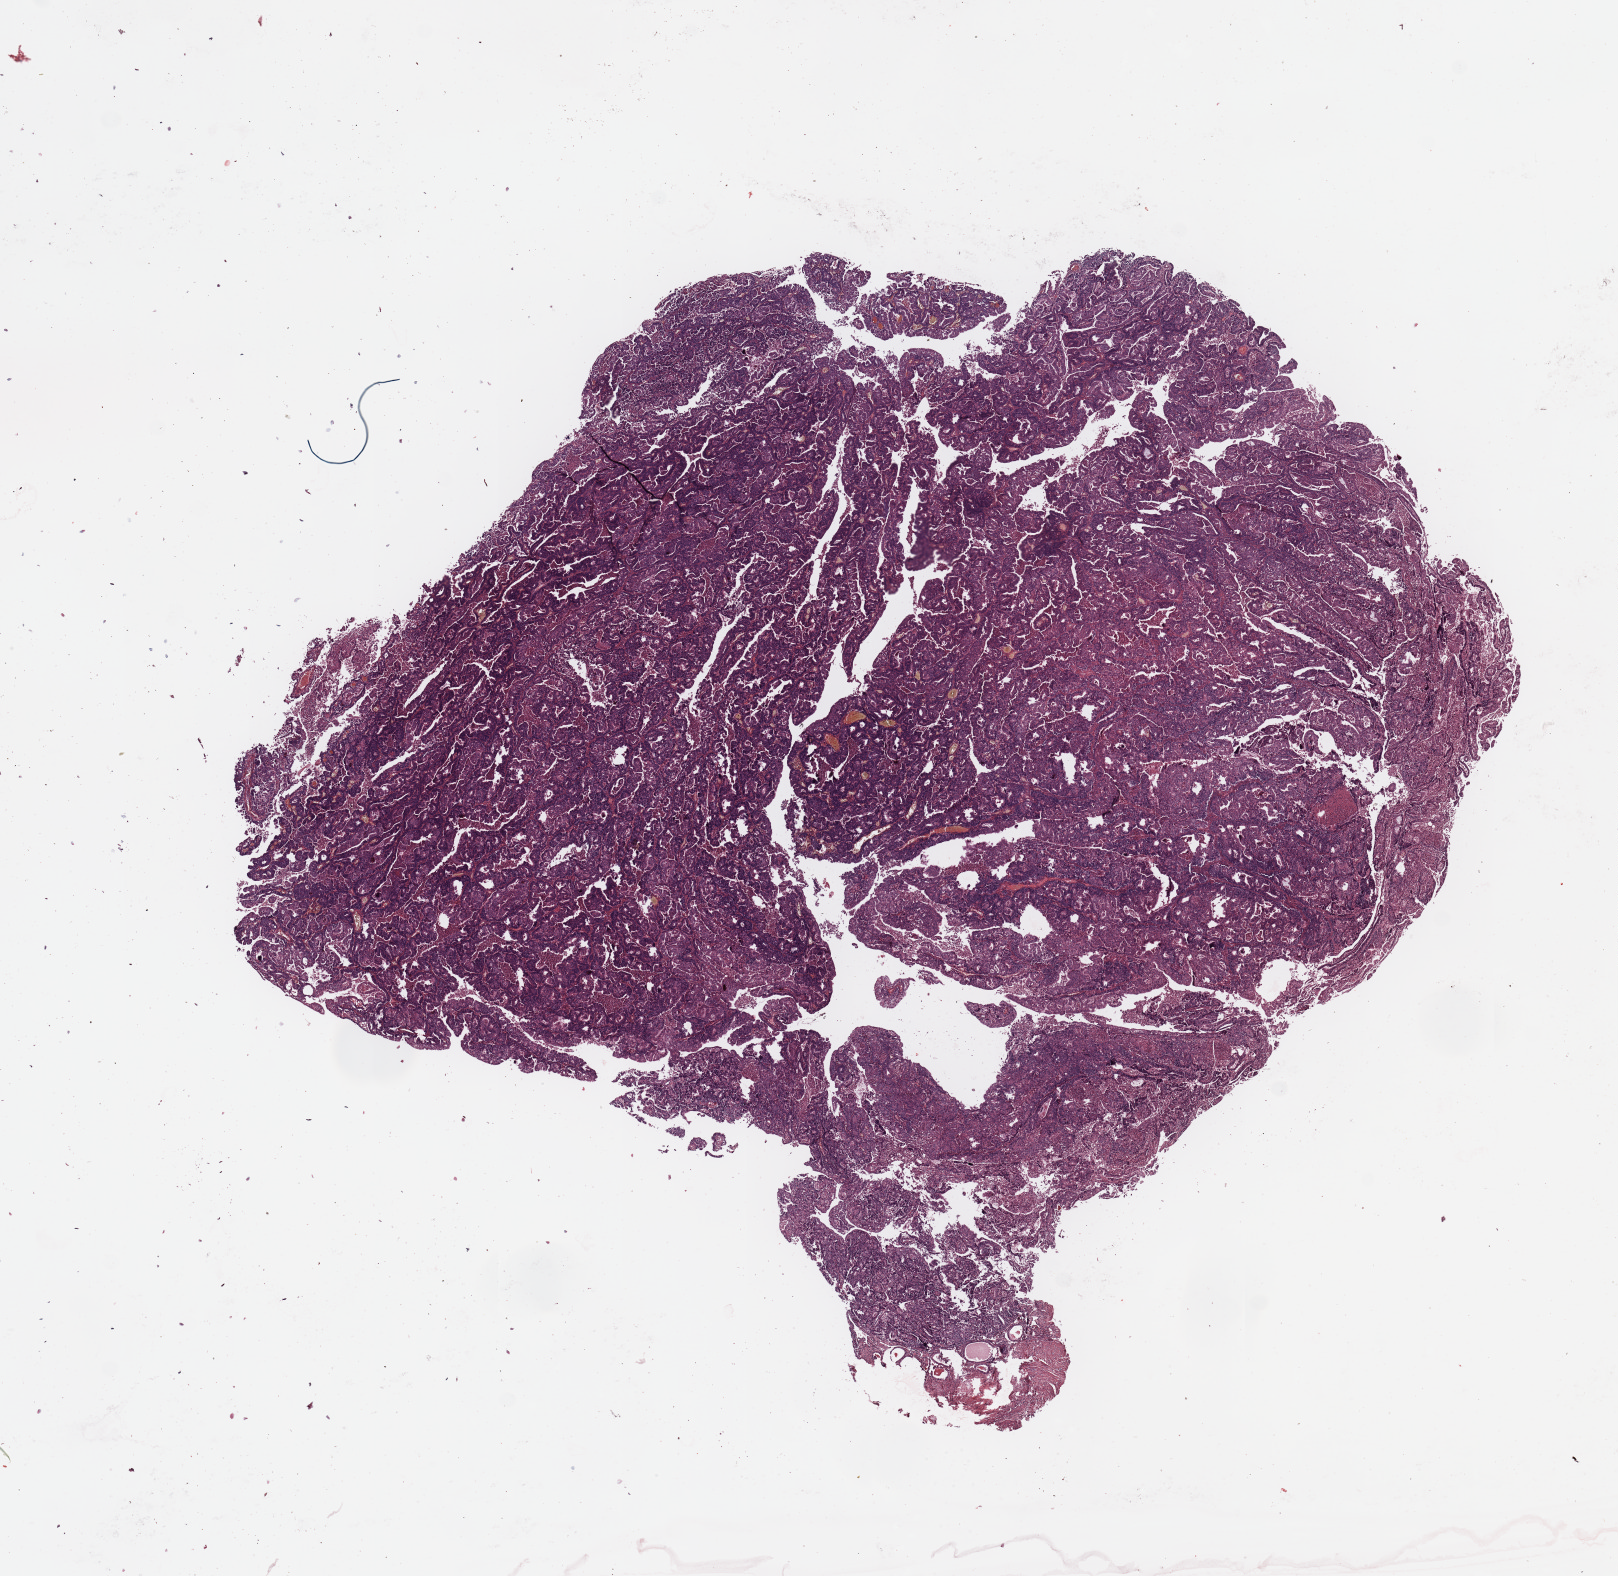
Whole-slide histology image, H&E — shown as a low-resolution overview of the whole scanned area (about 12.8 x 12.5 mm, acquisition: 20x scan). Tumour tissue sample, sampled site: uterus. Female, 77 y/o. Histologic grade: G2 (moderately differentiated). Composition of this section per pathologist review: tumour nuclei 98%, necrosis 0%.
- diagnosis: Endometrioid adenocarcinoma, NOS
- AJCC pathologic stage: I